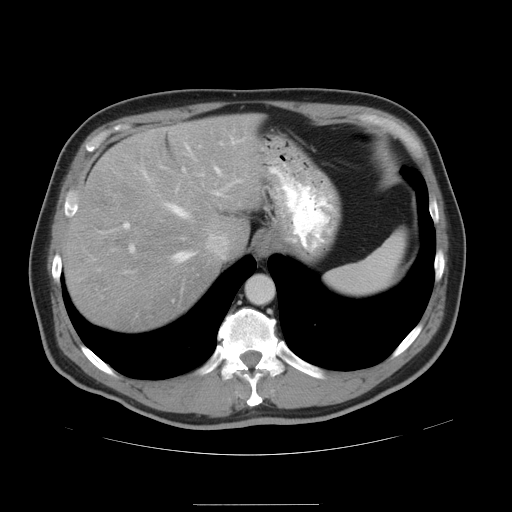
Contrast-enhanced abdominal CT, one axial slice. Position 37 of 47 along the scan axis. 120 kVp. Intravenous contrast given. Soft-tissue window (W 400 / L 40 HU). 5 mm slice thickness. 512 × 512 image matrix, field of view 420 × 420 mm. Male patient, age 61 years. Case-level facts recorded for this patient, not image findings: diagnosis: colorectal cancer liver metastases, imaged before liver resection; multiple liver metastases: no; largest metastasis: 1.2 cm; disease in both lobes: no.
Structures marked on this image (manually delineated by an expert):
- hepatic veins: bounding box [x1, y1, x2, y2] px = [164, 141, 237, 261]
- liver: [64, 115, 265, 332]
- planned liver remnant (the part of the liver to remain after resection): [64, 114, 265, 331]
- portal vein (with intrahepatic branches): [124, 168, 242, 251]